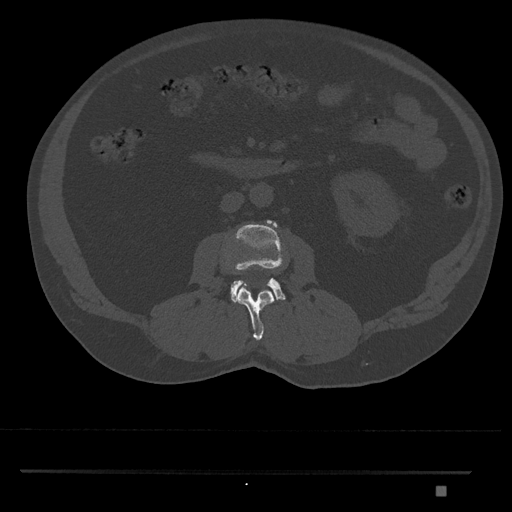
CT including the spine, one axial slice. Slice 719 of 1134 in the series (ordered by position). 120 kVp. Bone window (W 1800 / L 400 HU). 0.5 mm slice thickness. 512 × 512 image matrix, field of view 429 × 429 mm. Patient: male, 65 years. From the clinical record (not read from this slice): primary cancer: prostate.
Annotated regions visible in this slice (semi-automatically segmented with operator editing):
- L2 vertebra: bounding box (x1, y1, x2, y2) in pixels: (237, 286, 275, 341)
- L3 vertebra: (231, 220, 285, 303)